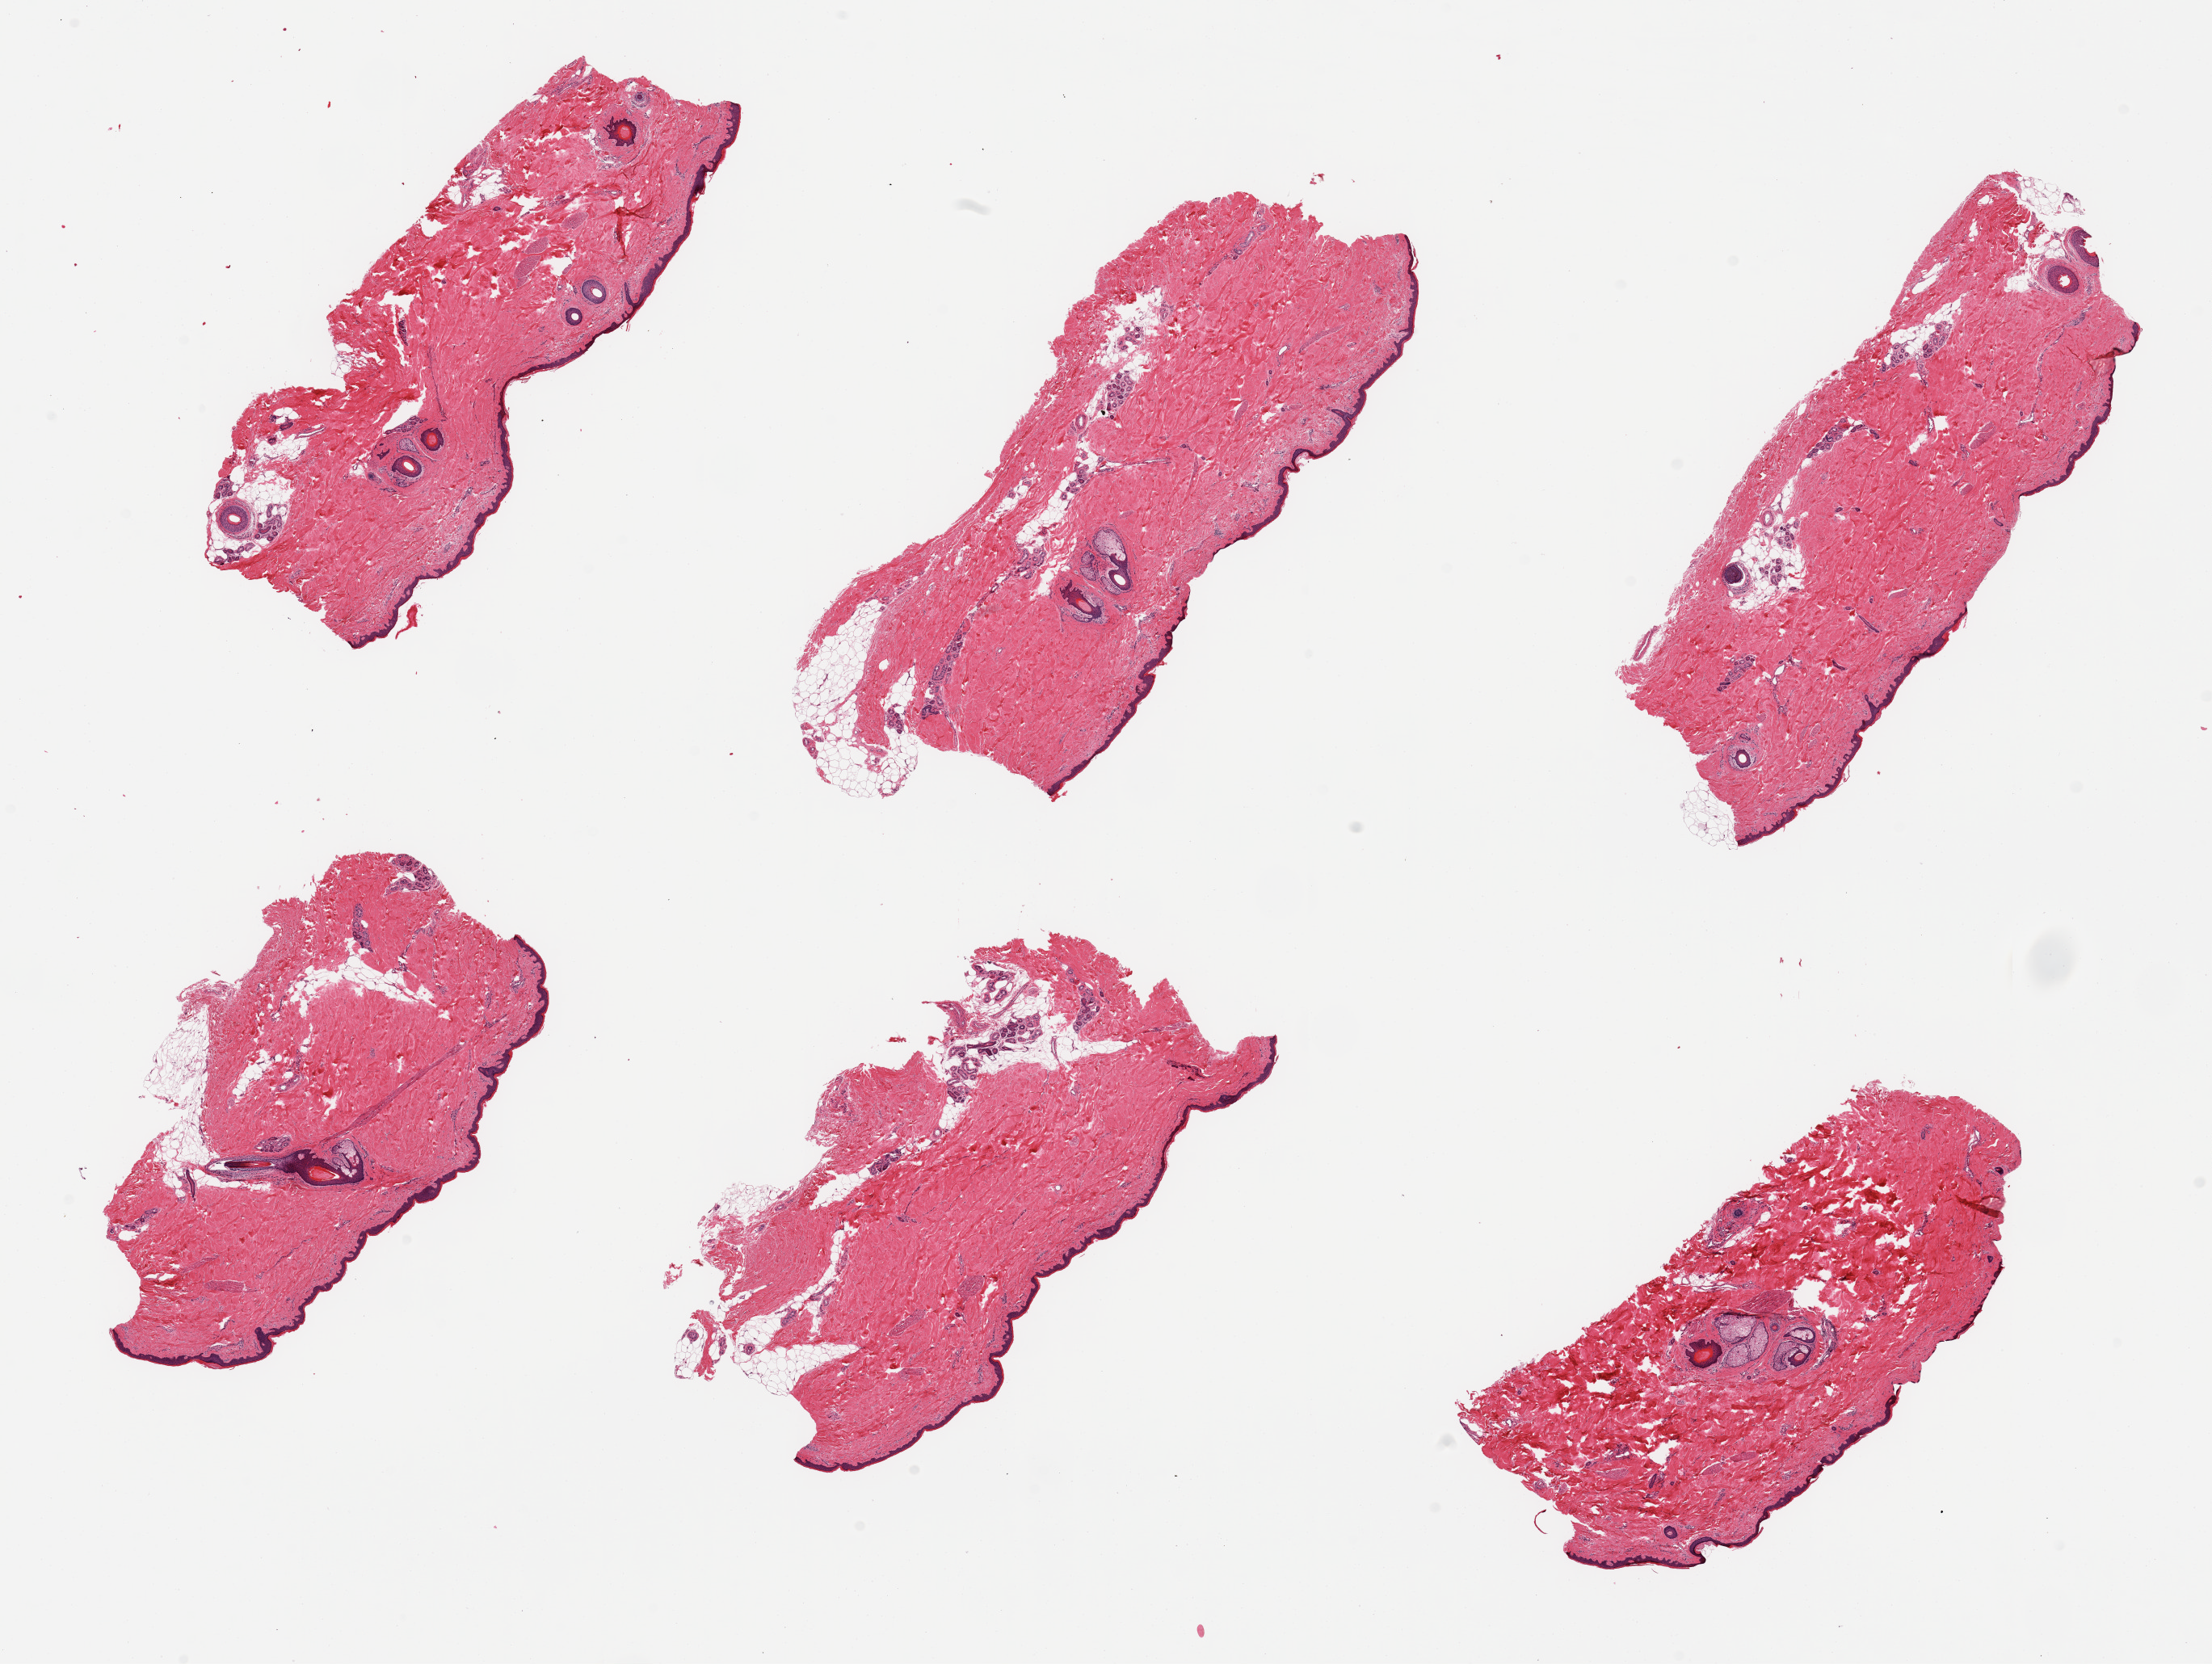
Digitized H&E-stained section, brightfield, a low-resolution overview of the entire scanned area, about 21.7 x 16.3 mm, PAXgene-fixed, paraffin-embedded tissue, section of skin of lower leg (target tissue), donor tissue sample. Donor sex: male.
Reviewer comment on this tissue sample: 6 pieces; well trimmed; 10% dermal fat.